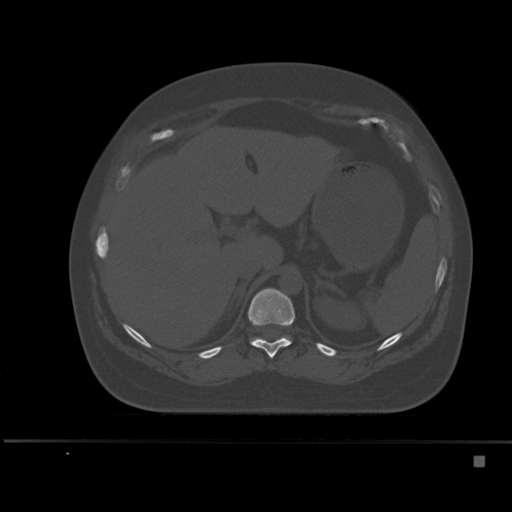
CT including the spine, one axial slice; slice 228 of 495 in the series (ordered by position); bone window (W 1800 / L 400 HU); 1.5 mm slice thickness; 512 × 512 image matrix, field of view 404 × 404 mm. Patient: female, 33 years. Case-level facts recorded for this patient, not image findings: primary cancer: breast; vertebrae with lytic lesions (as recorded): T1.
Outlined on this slice (semi-automatic segmentation, software-assisted and operator-edited):
- T11 vertebra: bounding box [x1, y1, x2, y2] px = [248, 288, 295, 358]
- T12 vertebra: [251, 336, 290, 342]